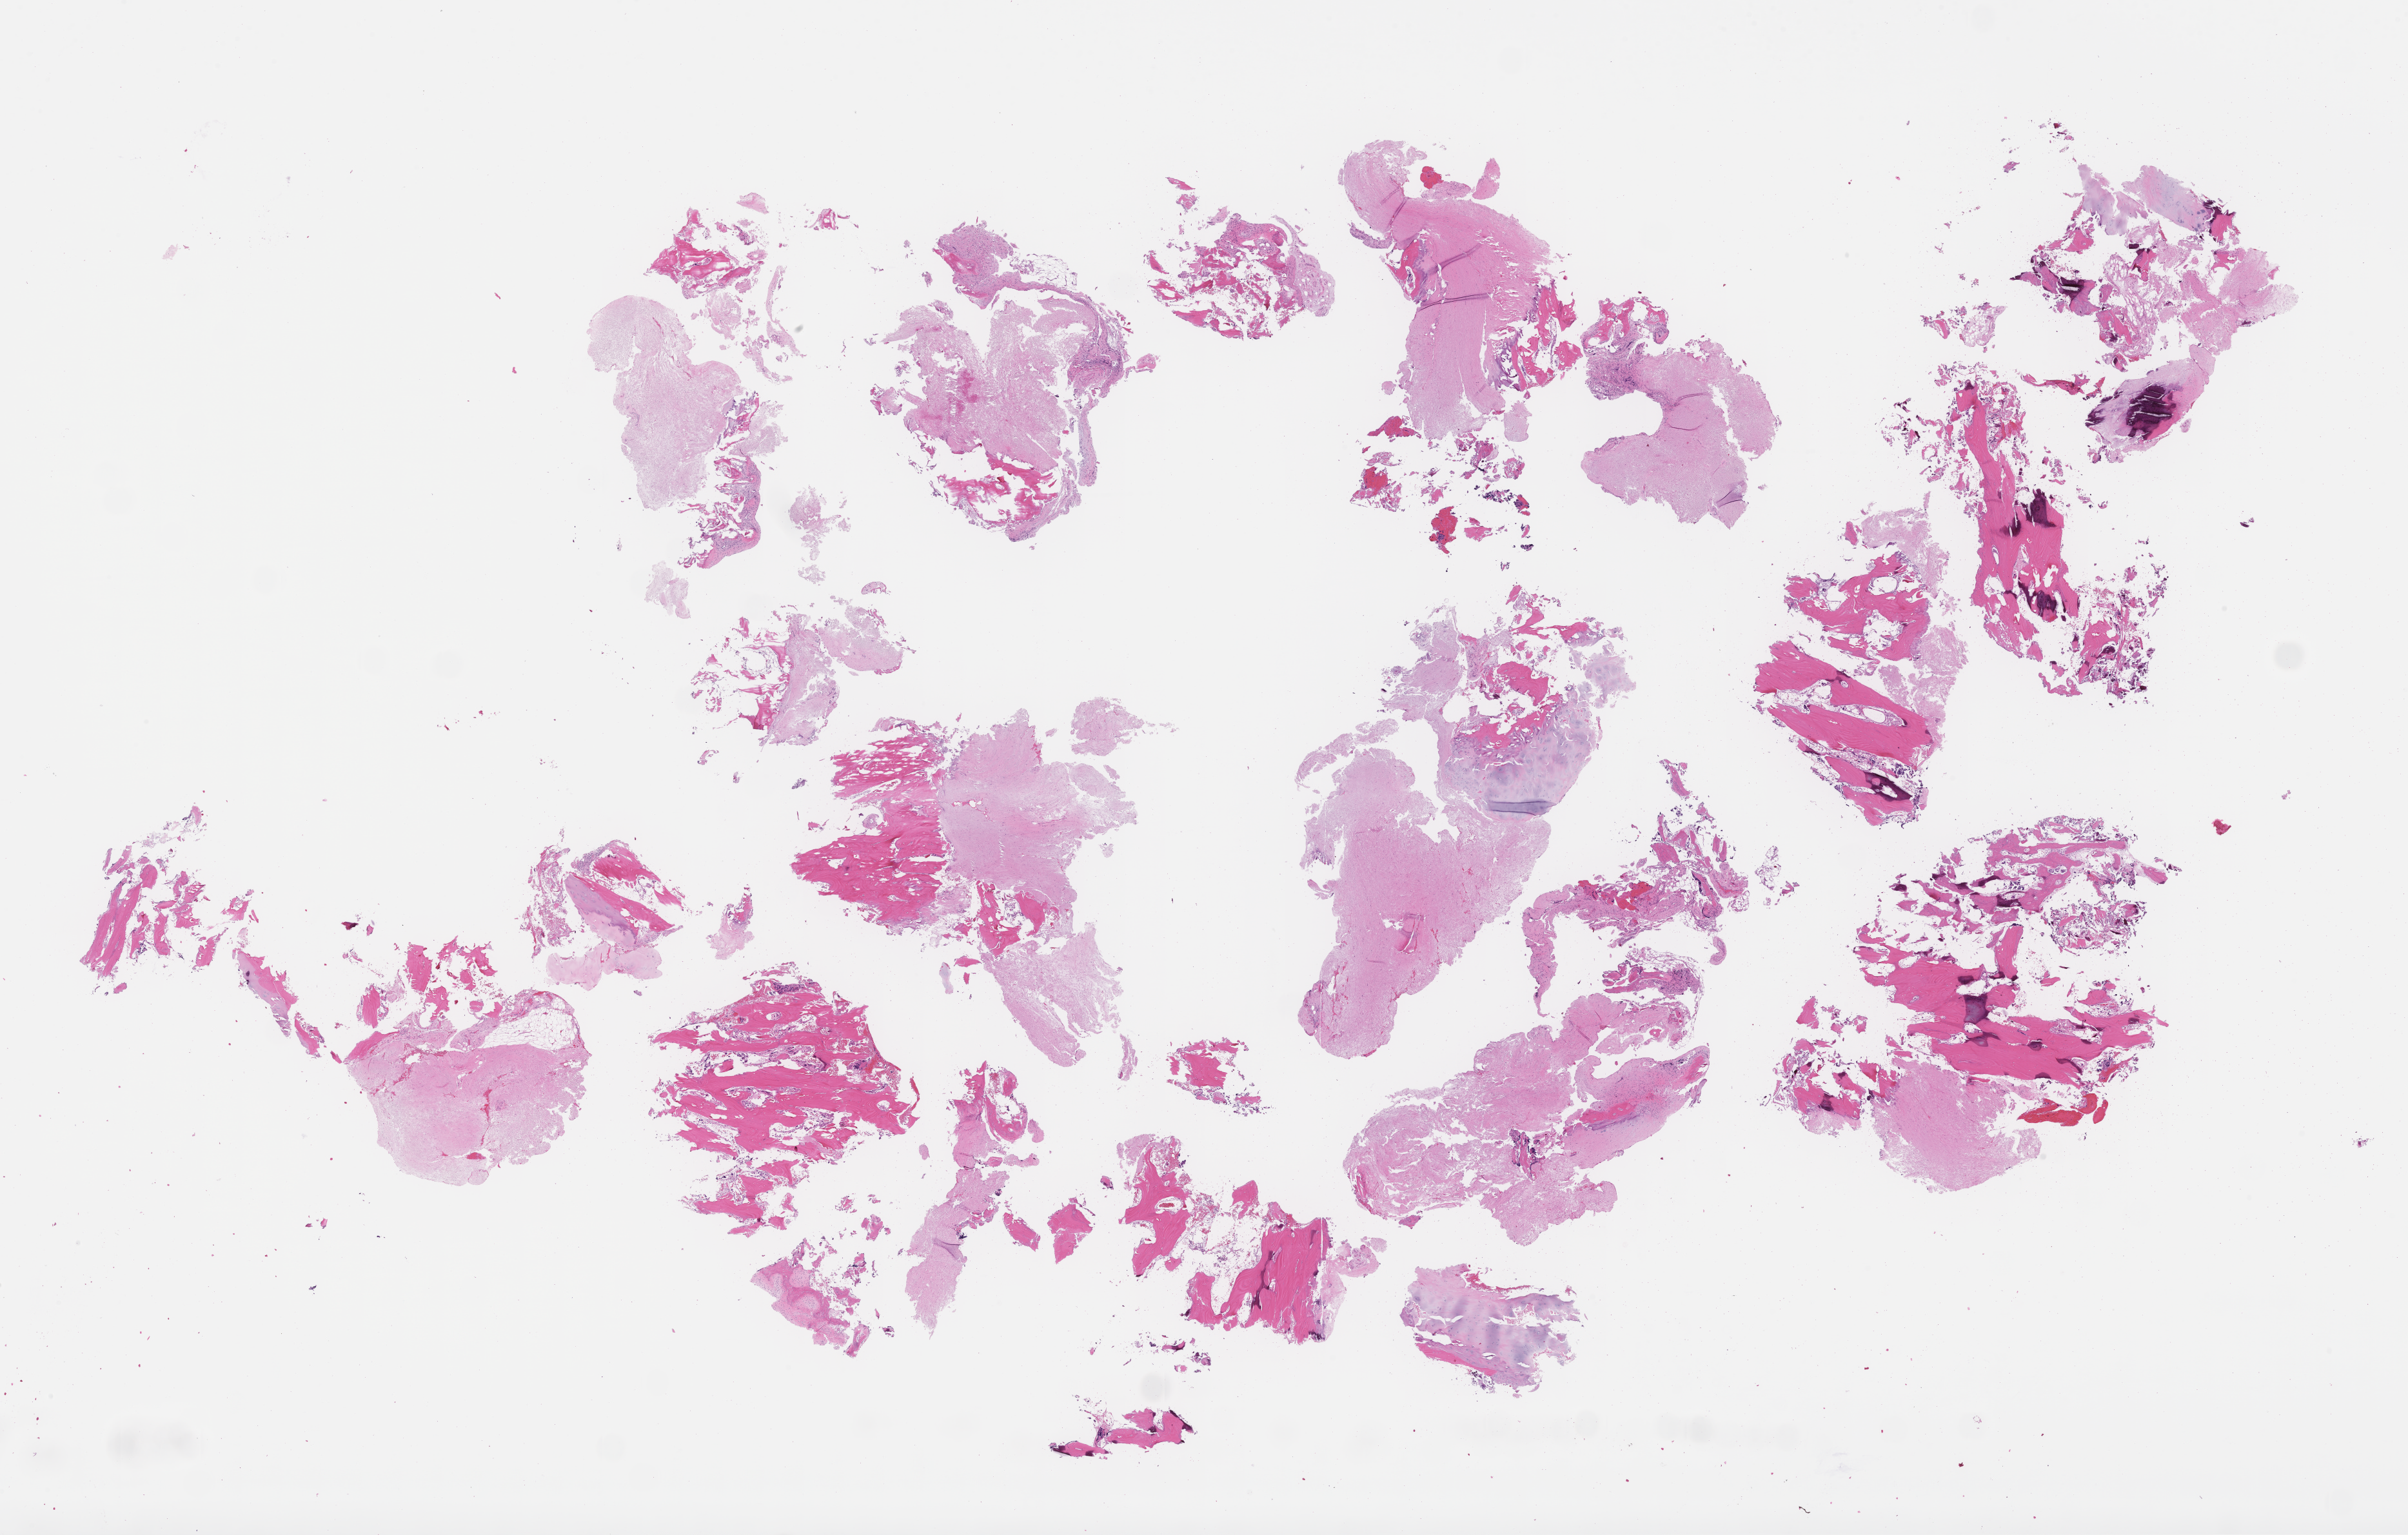
Whole-slide image, haematoxylin and eosin stain, shown as a low-resolution overview of the whole scanned area (about 30.2 x 19.2 mm), formalin-fixed, paraffin-embedded (FFPE) tissue. Patient sex: male.
This section: metastasis (sampled organ not recorded). Patient diagnosis (primary): Prostate Carcinoma.